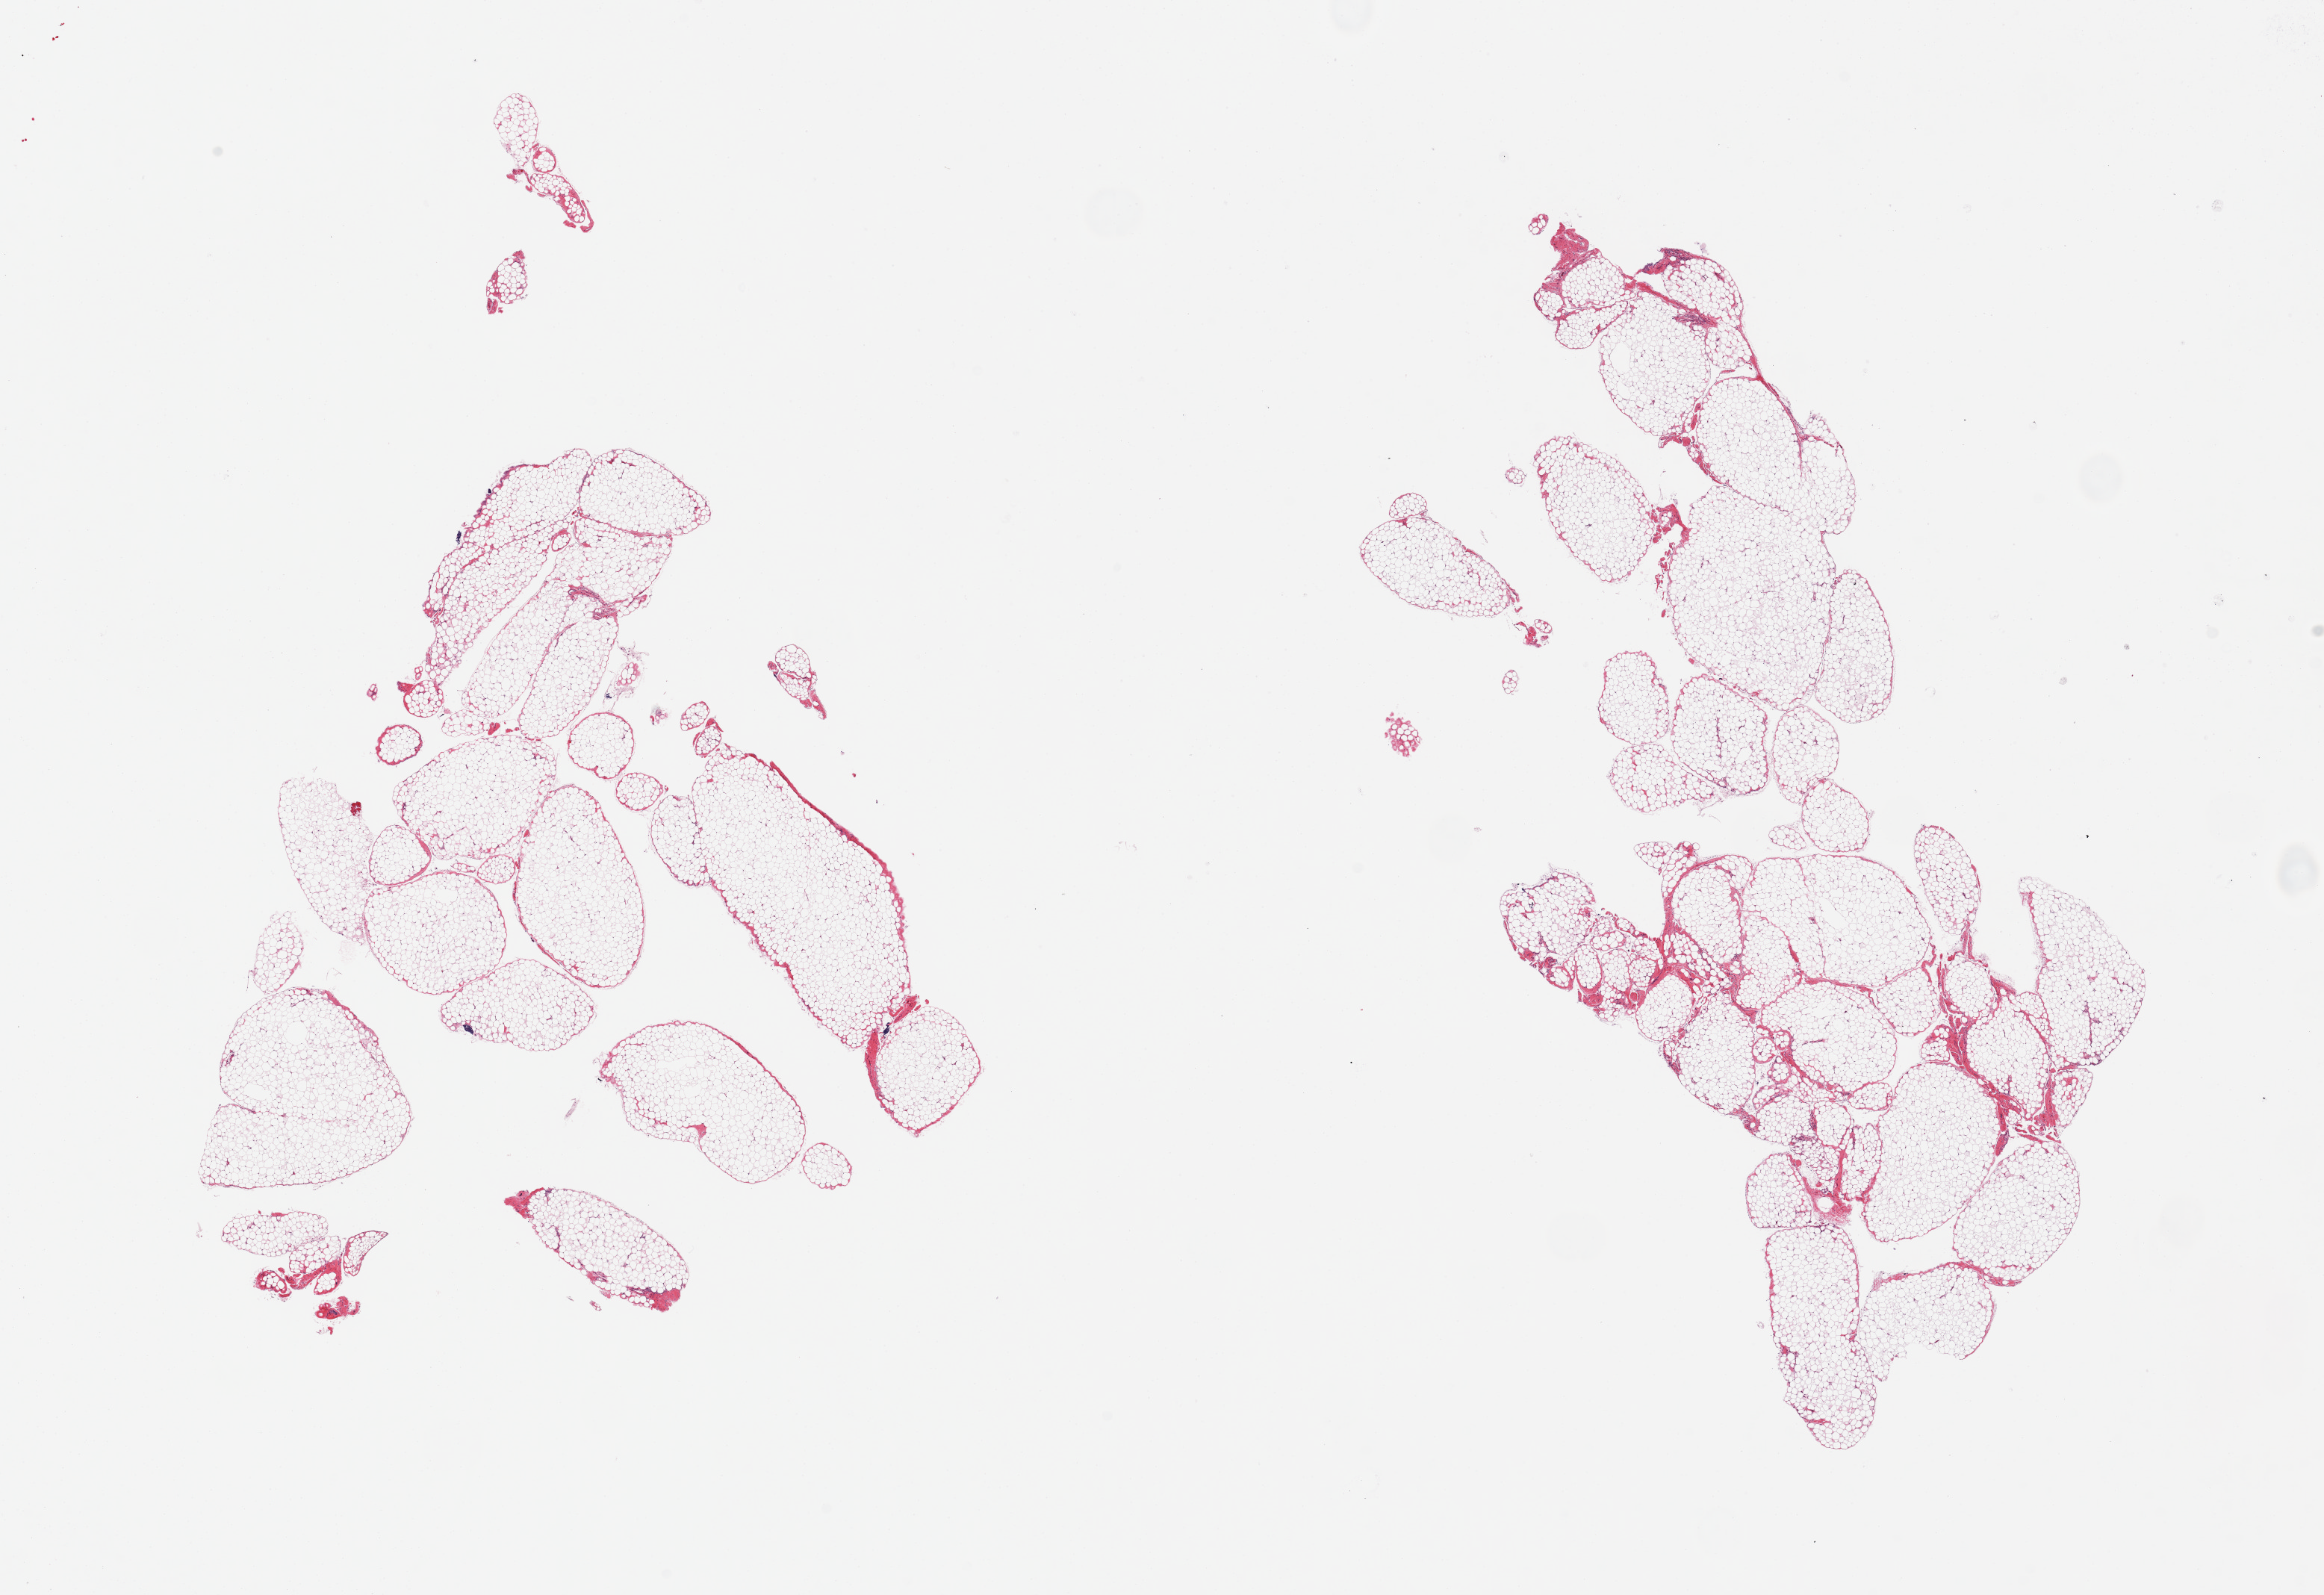
Digitized hematoxylin and eosin (H&E)-stained section, brightfield — low-resolution overview of the scanned area, about 24.6 x 16.9 mm (slide scanned at 20x); PAXgene-fixed paraffin-embedded (PFPE) section; target tissue: omentum; donor tissue sample. Female donor.
* review note (as recorded): 2 pieces, no abnormalities, minimal fascia/fibrous tissue